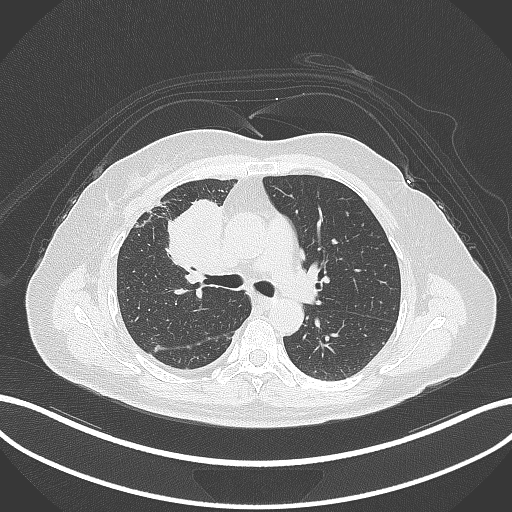
Chest CT, one axial slice; slice 176 of 305 in the series (ordered by position); reconstruction kernel B70f; 120 kVp; lung window (W 1500 / L -600 HU); 1 mm slice thickness; 512 × 512 image matrix, field of view 400 × 400 mm. Female patient, age 52 years. Case-level facts recorded for this patient, not image findings: clinical TNM (as recorded): T3 N1 M1.
Annotated regions visible in this slice (bounding box drawn by a radiologist):
- lung tumour (recorded histology: adenocarcinoma): bounding box <166,195,223,279> (left, top, right, bottom; pixels)